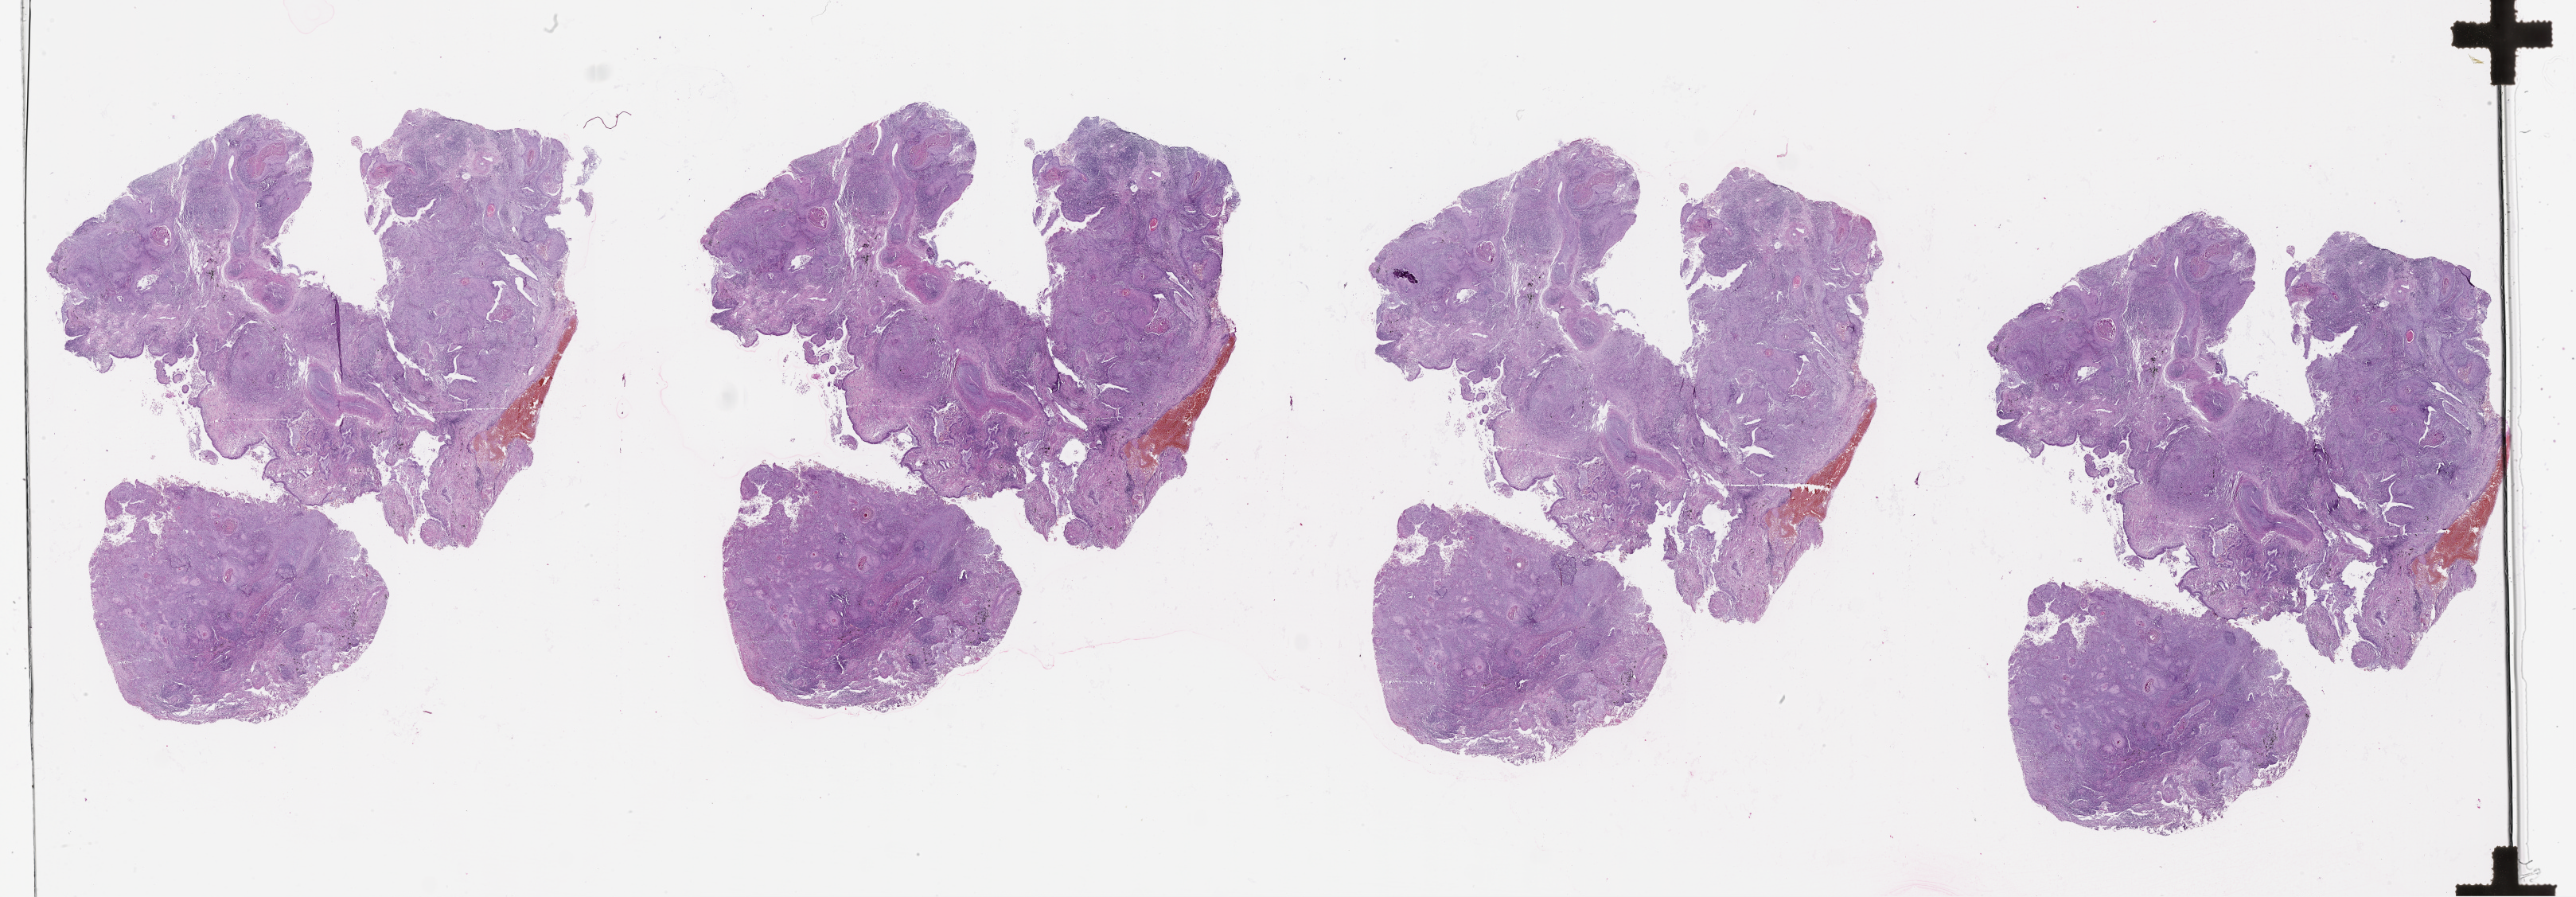
Whole-slide histology image, H&E-stained — low-resolution overview of the scanned area, about 52.1 x 18.1 mm (slide scanned at 20x); lung, tumour tissue. Patient: male, age 72 years.
- patient diagnosis (cohort enrolment): squamous cell carcinoma (lung)